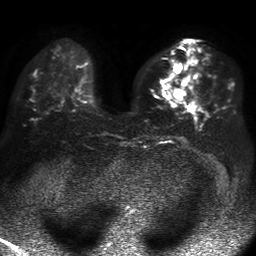
Breast MRI, one axial slice. Position 20 of 50 along the scan axis. Diffusion-weighted series; image 2 of 4 stored at this slice position (different b-values; order by instance number). 1.5 T. 4 mm slice thickness. 256 × 256 image matrix. Female patient.
Annotated regions visible in this slice (outlined manually by an expert reader):
- tumour on diffusion-weighted imaging: bounding box [x1, y1, x2, y2] px = [170, 60, 186, 100]